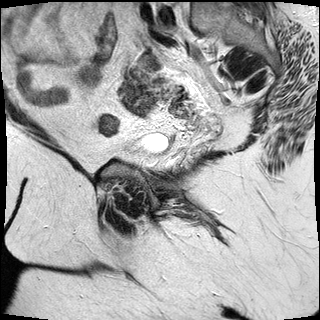
Pelvic MRI for cervical cancer, one sagittal slice; T2-weighted; 1.5 T; TE 89 ms, TR 2930 ms; 4 mm slice thickness; 320 × 320 image matrix, field of view 260 × 260 mm. Female patient, age 53 years.
Outlined on this slice (manually delineated by an expert):
- uterus and cervix: bounding box <119,73,158,116> (left, top, right, bottom; pixels)